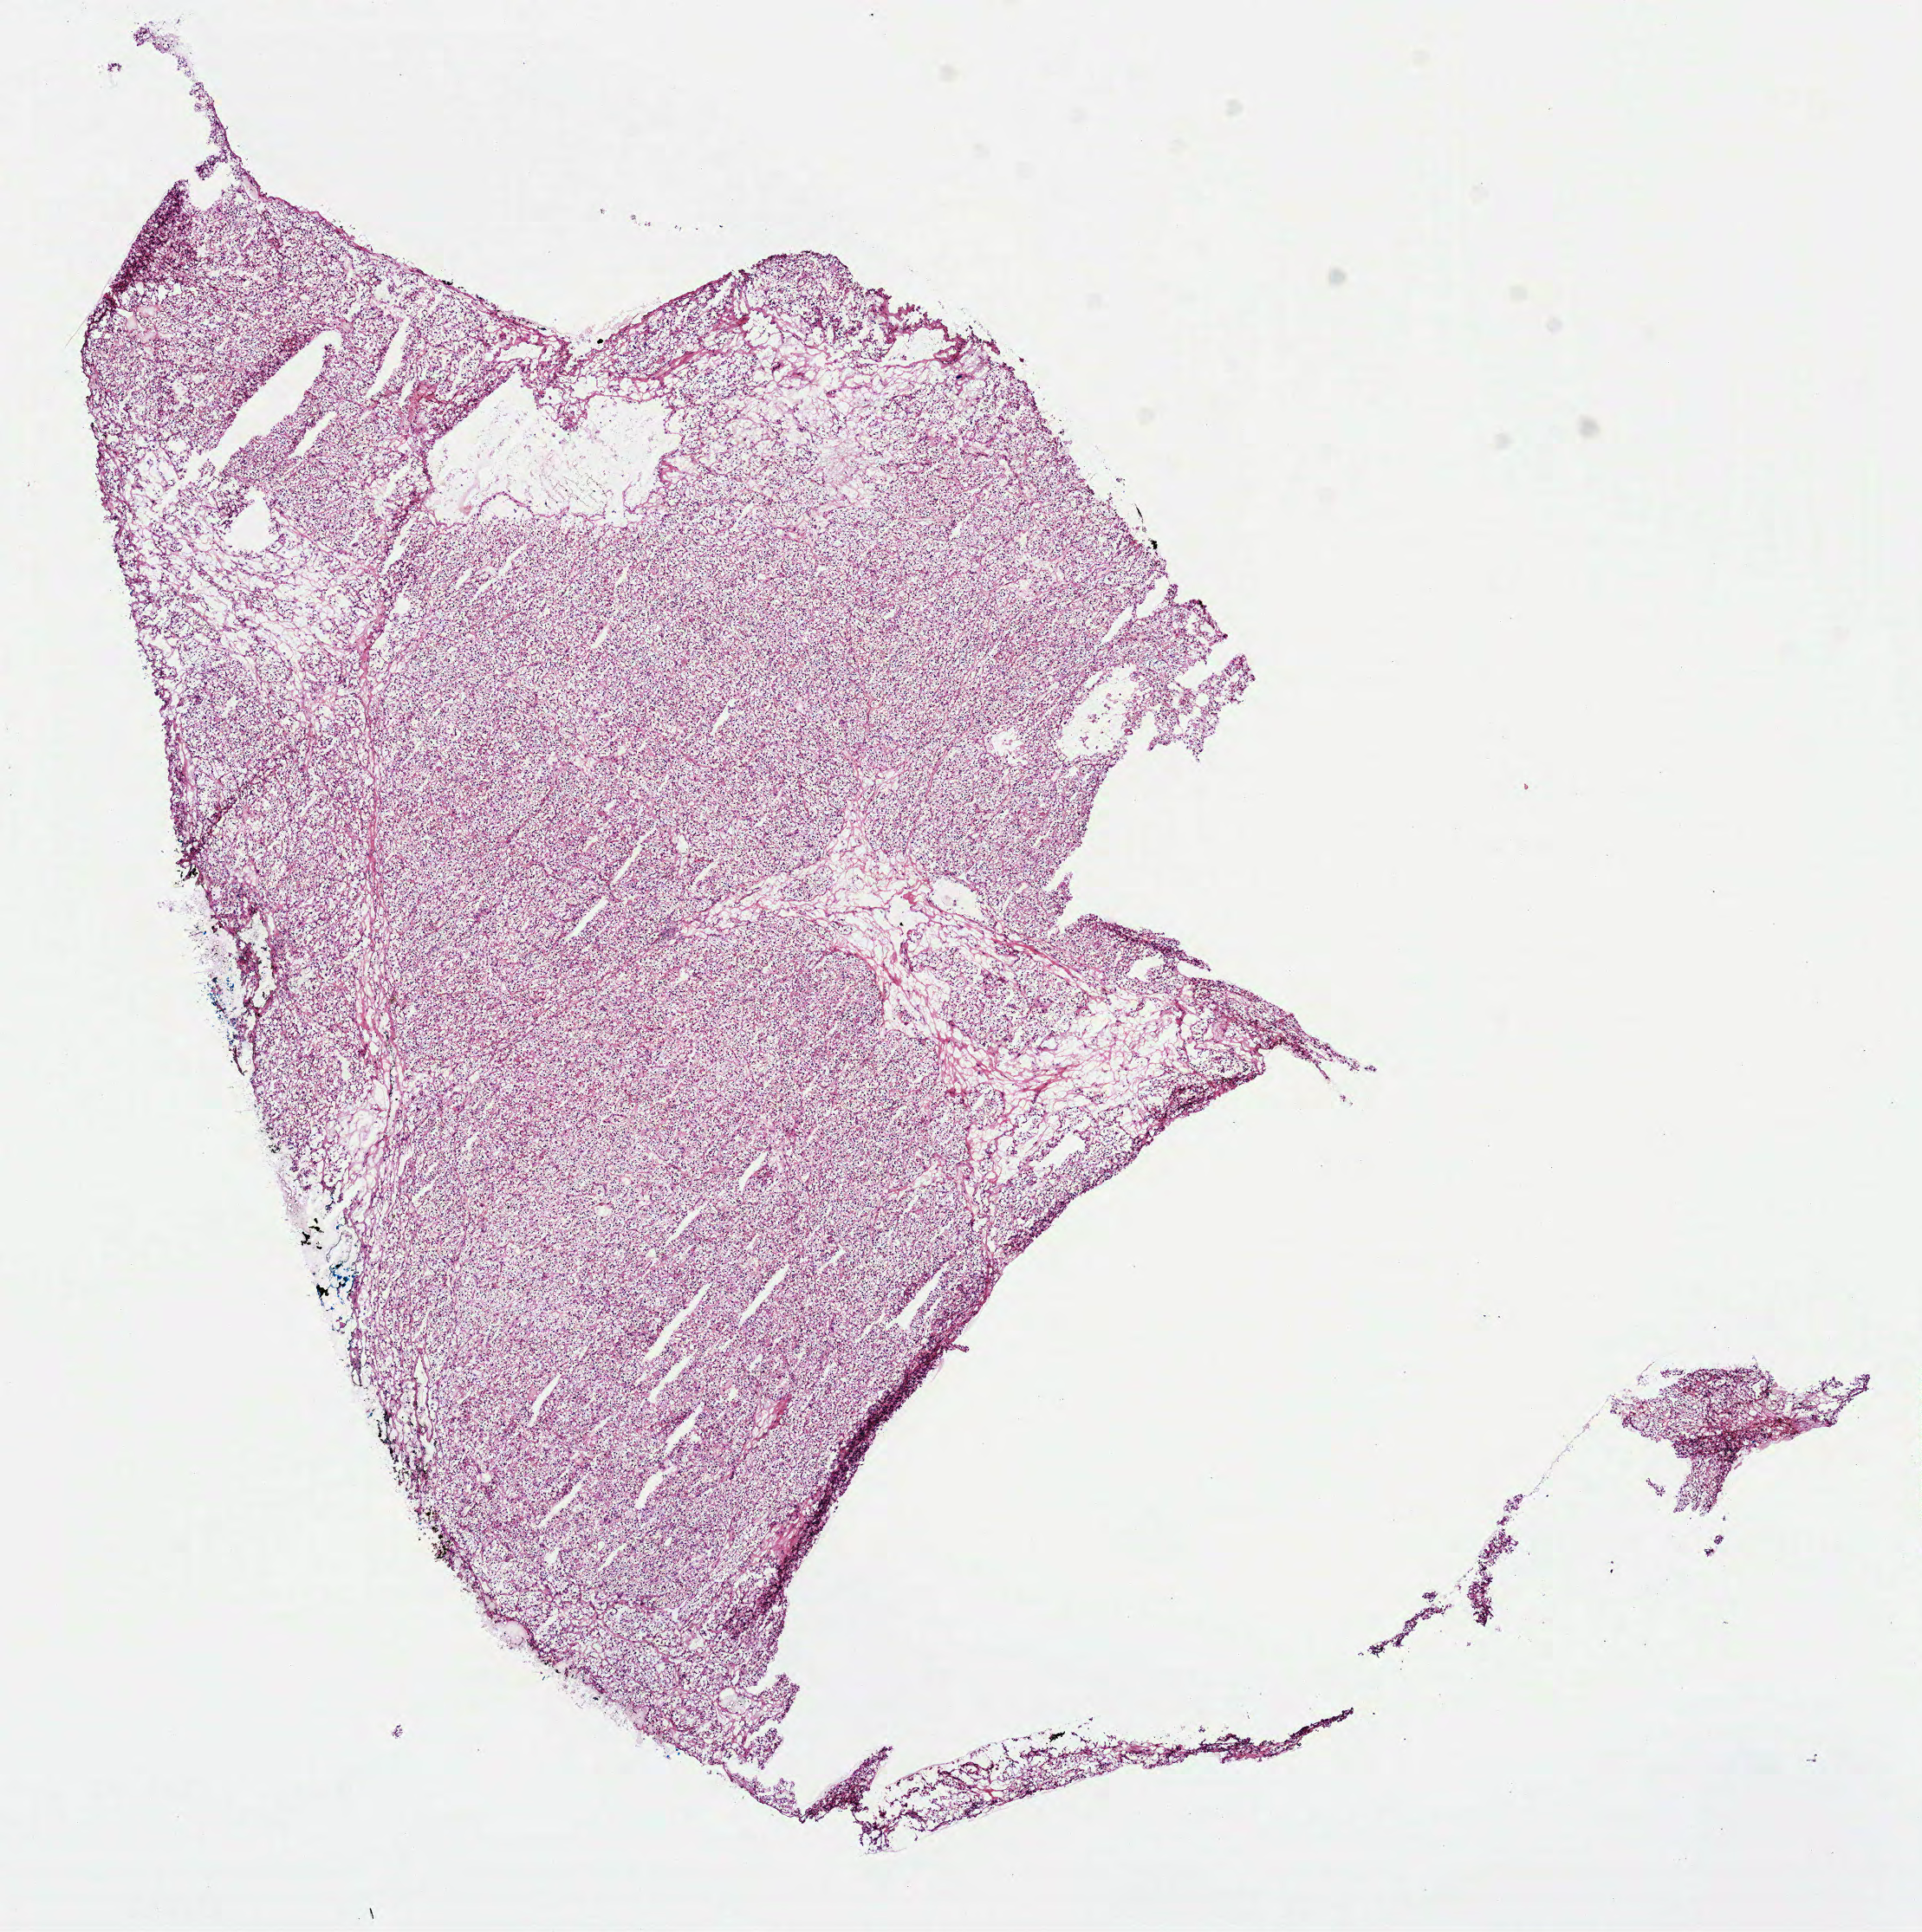
Whole-slide histology image, Hematoxylin and eosin (H&E) stained, a low-resolution overview of the entire scanned area, about 8.9 x 9.0 mm (acquisition: 40x scan), frozen section, sample: primary tumour, kidney. Male, age 75 years at initial diagnosis. Histologic grade: G2 (moderately differentiated). Slide review estimates, as recorded: tumour cells 100%, tumour nuclei 75%, normal cells 0%, stromal cells 0%, necrosis 0%. Inflammatory infiltration, as recorded: lymphocyte infiltration 2%, monocyte infiltration 3%, neutrophil infiltration 0%.
* diagnosis: Clear cell adenocarcinoma, NOS
* AJCC pathologic stage: I (7th edition)
* laterality: right